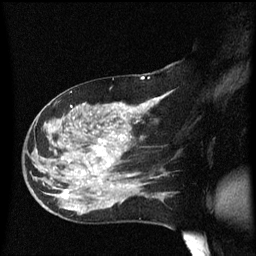
Breast MRI (dynamic contrast-enhanced), one sagittal slice; position 31 of 60 along the scan axis; dynamic contrast-enhanced series, image 2 of 3 at this slice position (ordered by acquisition); 1.5 T; TE 4.2 ms, TR 8.4 ms; 2.2 mm slice thickness; 256 × 256 image matrix. Patient: female, 47 years.
Outlined on this slice (semi-automatic segmentation, software-assisted and operator-edited):
- analysis volume of interest (the breast-tissue region the enhancement analysis was run in; not a lesion): box from (x=24, y=97) to (x=149, y=206) px
- tumour enhancement mask (voxels above the 70 % enhancement threshold inside the analysis volume of interest): (x=62, y=102)–(x=149, y=199)